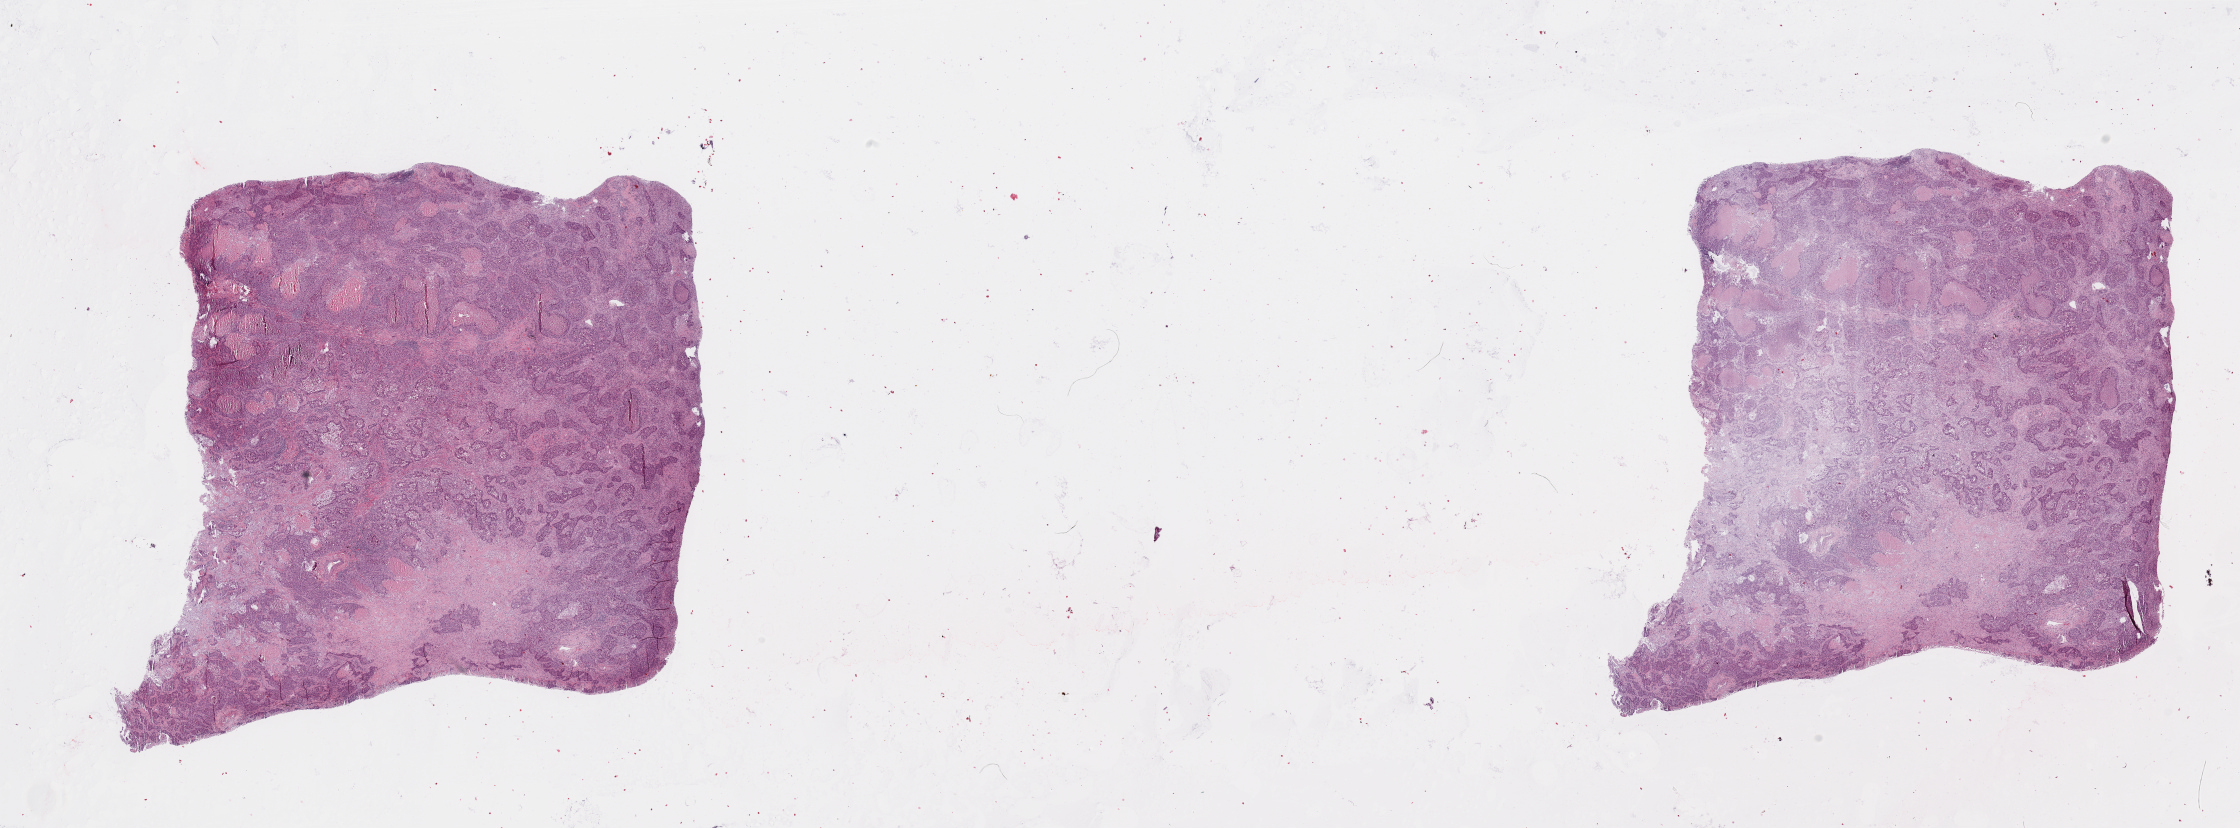
H&E whole-slide image — whole scanned area (about 35.4 x 13.1 mm) shown as a low-resolution overview. Tumour tissue sample, sampled site: lung. 62-year-old male patient. Histologic grade: G3 (poorly differentiated). Pathologist review of this section (percent, as recorded): tumour nuclei 65%, necrosis 20%.
• primary tumour site (as recorded): left lower lobe
• AJCC pathologic stage: IIIB
• histologic diagnosis: Squamous cell carcinoma, NOS